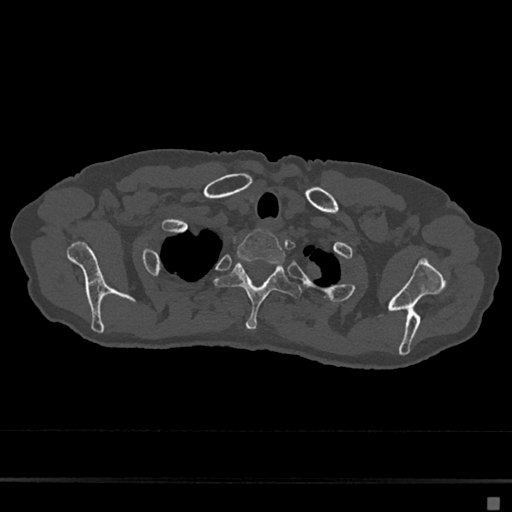
CT including the spine, one axial slice. Bone window (W 1800 / L 400 HU). 512 × 512 image matrix, field of view 360 × 360 mm. Female patient, age 68 years. From the clinical record (not read from this slice): primary cancer: renal.
Outlined on this slice (semi-automatic segmentation, software-assisted and operator-edited):
- T1 vertebra: bounding box [x1, y1, x2, y2] px = [236, 230, 286, 263]
- T2 vertebra: [215, 262, 302, 331]